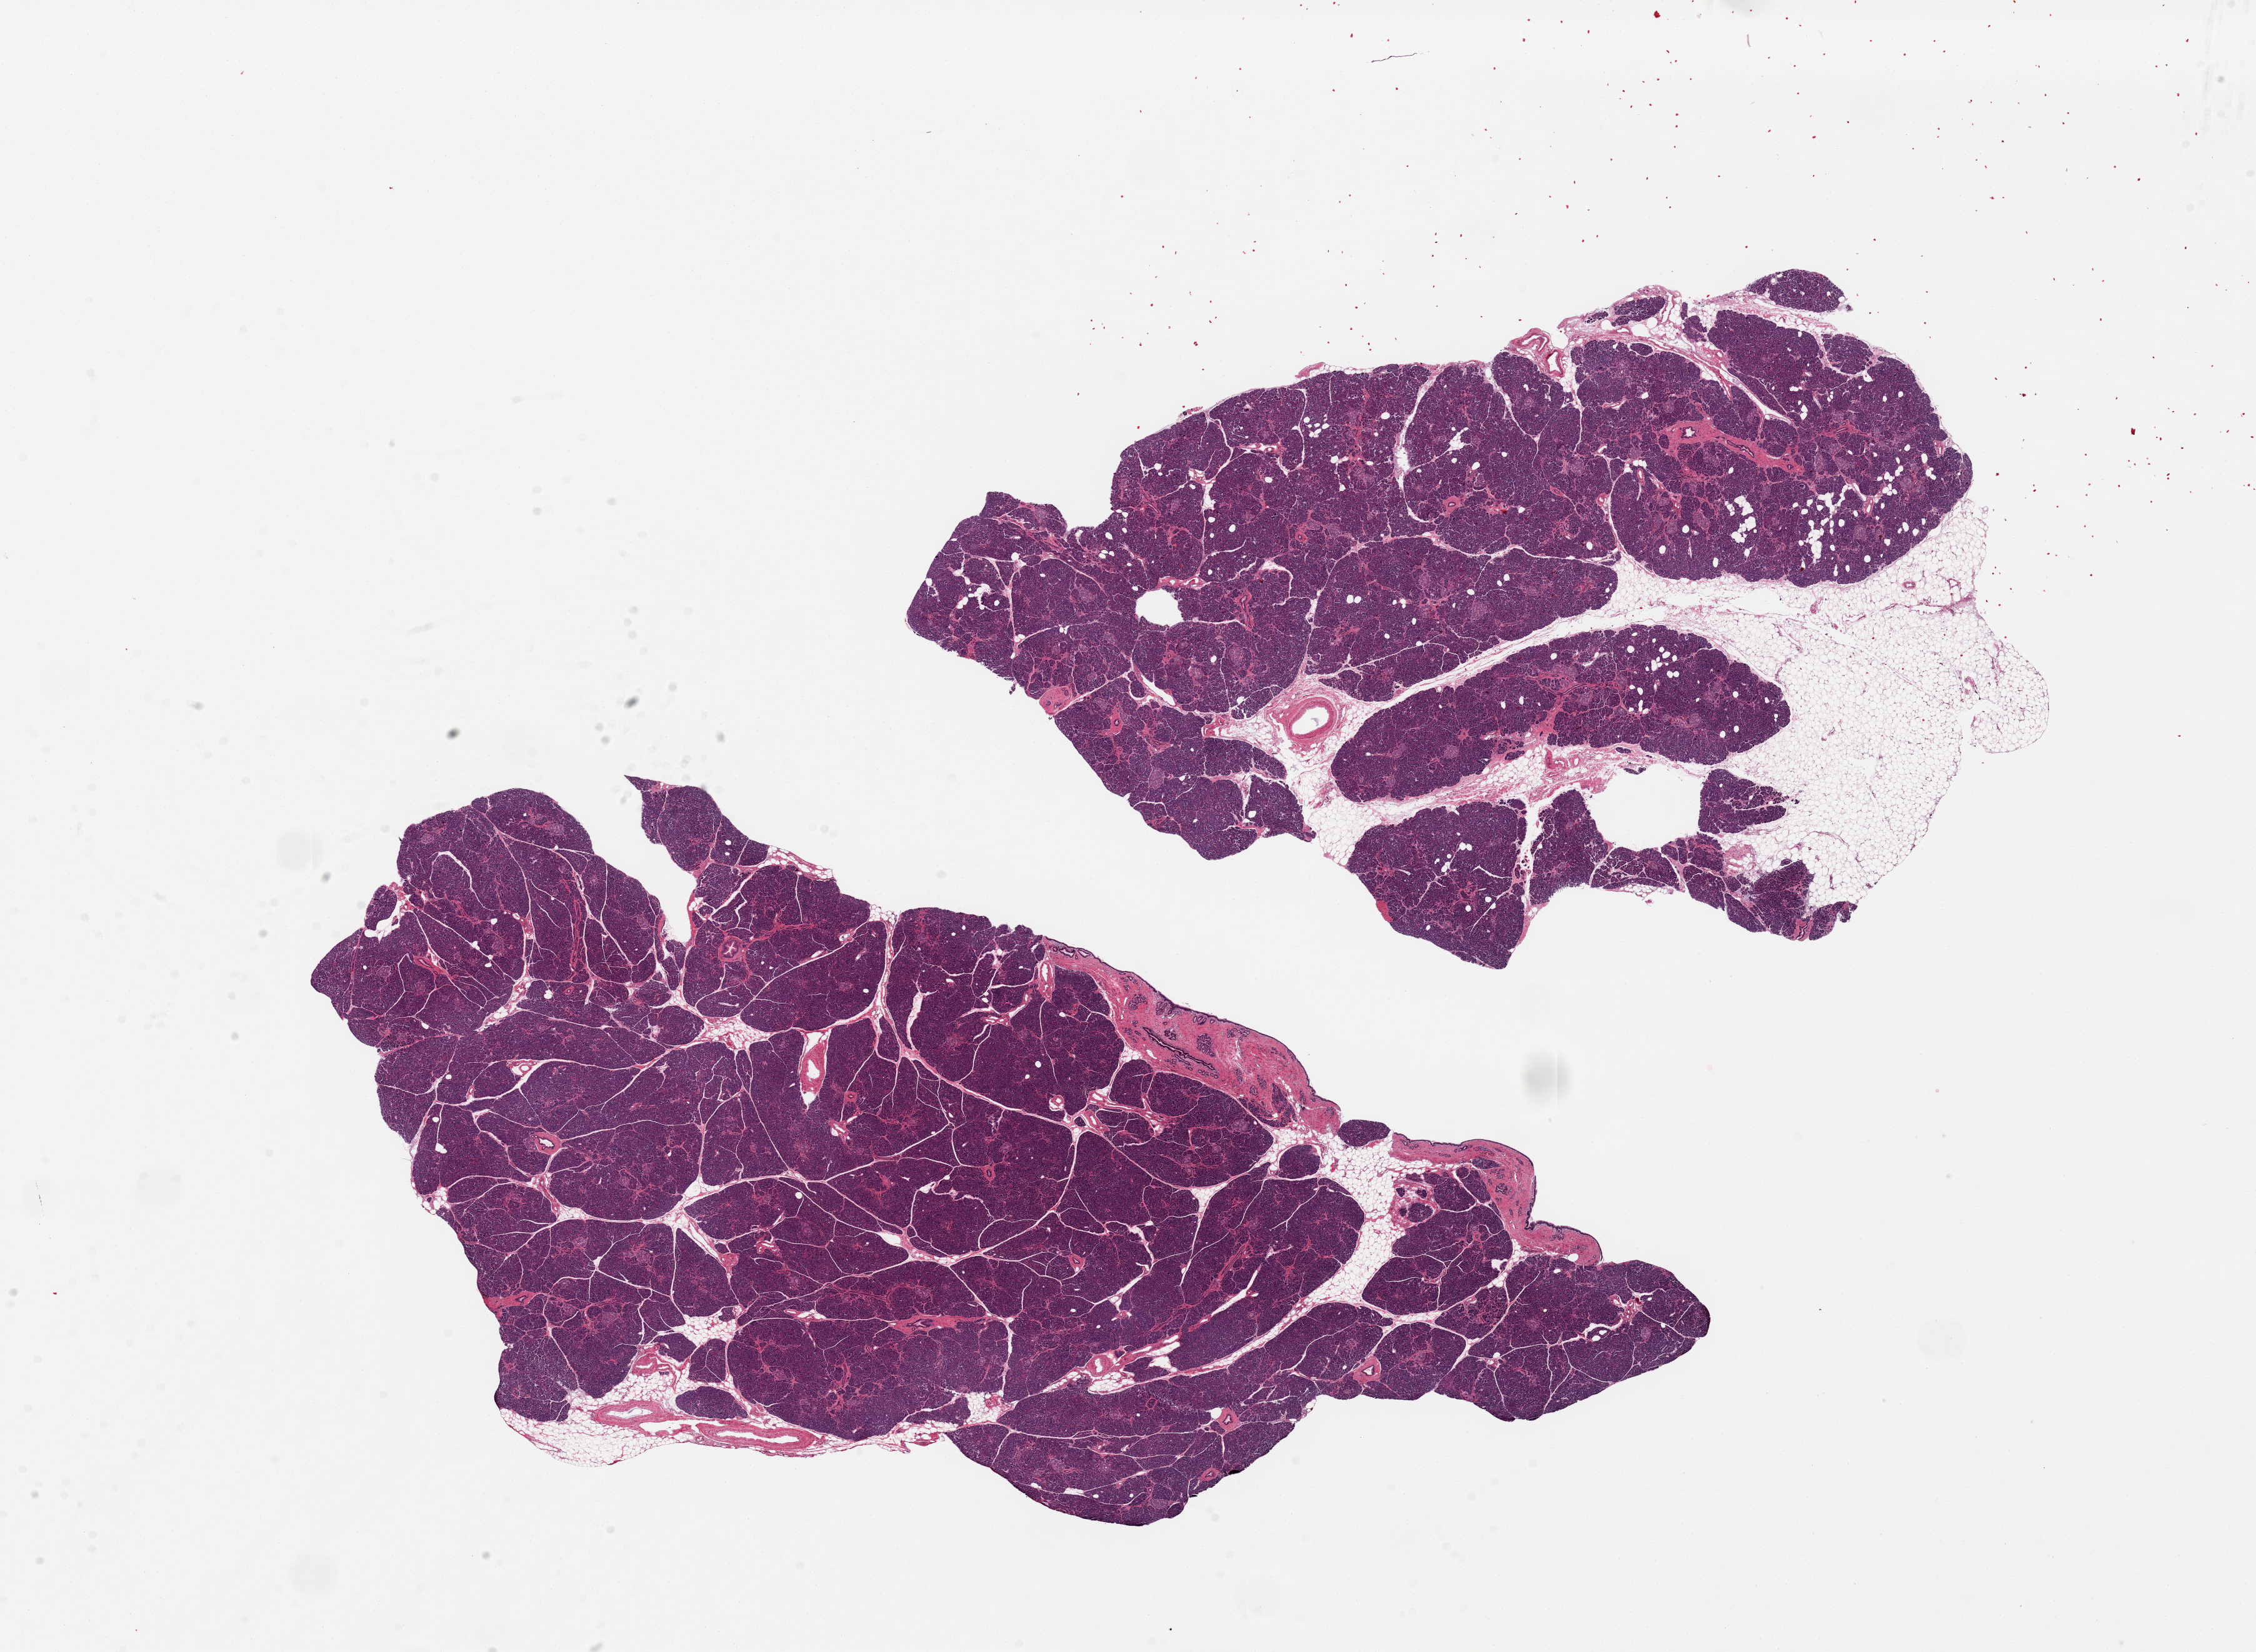
Whole-slide image, hematoxylin and eosin (H&E) stain, shown as a low-resolution overview of the whole scanned area (about 28.5 x 20.9 mm). PAXgene-fixed, paraffin-embedded tissue. Section of pancreas (target tissue). Tissue donor sample. Female donor.
Pathologist's review note for this sample: 2 pieces. 18x9 & 13x10mm; 1 has 25% adipose.